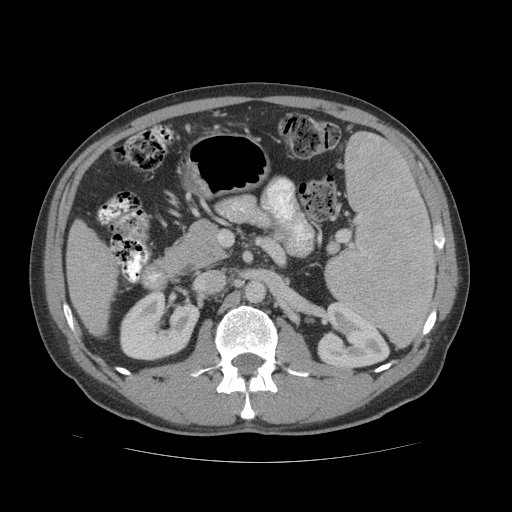
Contrast-enhanced abdominal CT (liver protocol), one axial slice. Slice 18 of 81 in the series (ordered by position). Reconstruction kernel STANDARD. Soft-tissue window (W 400 / L 40 HU). 2.5 mm slice thickness. 512 × 512 image matrix. Case-level facts recorded for this patient, not image findings: diagnosis: hepatocellular carcinoma (patient treated with transarterial chemoembolisation; whether this scan precedes or follows treatment is not stated here); TNM stage (as recorded): Stage-IVB; Child-Pugh class: B; tumour differentiation: well differentiated; tumour nodularity: multinodular.
Annotated regions visible in this slice (semi-automatic segmentation, software-assisted and operator-edited):
- liver parenchyma outside the tumour (the mass and vessels are separate outlines, so this box may not span the whole liver): bounding box [x1, y1, x2, y2] px = [66, 220, 118, 334]